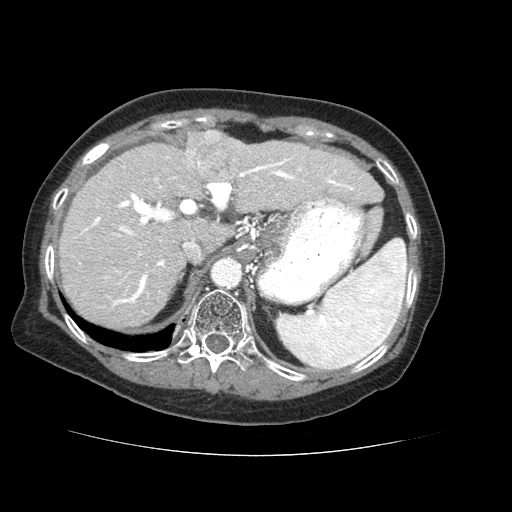
Contrast-enhanced abdominal CT (liver protocol), one axial slice. Soft-tissue window (W 400 / L 40 HU). 512 × 512 image matrix, field of view 360 × 360 mm. Case-level facts recorded for this patient, not image findings: diagnosis: hepatocellular carcinoma (patient treated with transarterial chemoembolisation; whether this scan precedes or follows treatment is not stated here); TNM stage (as recorded): Stage-IVB; Child-Pugh class: A; tumour differentiation: well differentiated; tumour nodularity: uninodular.
Outlined on this slice (semi-automatic segmentation, software-assisted and operator-edited):
- liver parenchyma outside the tumour (the mass and vessels are separate outlines, so this box may not span the whole liver): box from (x=58, y=130) to (x=382, y=328) px
- mass: (x=183, y=130)–(x=245, y=181)
- liver vessels: (x=81, y=157)–(x=354, y=306)